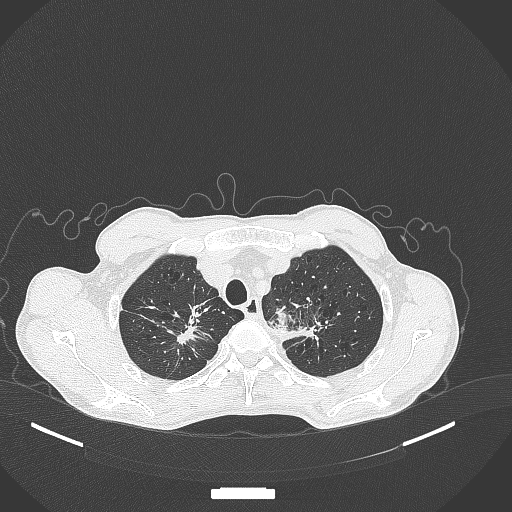
Chest CT, one axial slice. Slice 366 of 386 in the series (ordered by position). Reconstruction kernel B70f. Lung window (W 1500 / L -600 HU). 1 mm slice thickness. 512 × 512 image matrix, field of view 400 × 400 mm. Male patient, age 65 years. From the clinical record (not read from this slice): clinical TNM (as recorded): T2b N0 M0; histopathological grade: G2.
Annotated regions visible in this slice (bounding box drawn by a radiologist):
- lung tumour (recorded histology: adenocarcinoma): bounding box (x1, y1, x2, y2) in pixels: (270, 307, 297, 329)